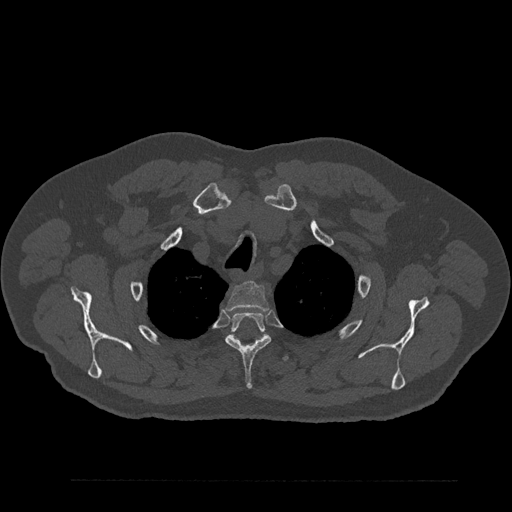
CT including the spine, one axial slice. Position 685 of 797 along the scan axis. Reconstruction kernel Br40s/3. 120 kVp. Bone window (W 1800 / L 400 HU). 0.5 mm slice thickness. 512 × 512 image matrix, field of view 430 × 430 mm. Male patient, age 61 years. From the clinical record (not read from this slice): primary cancer: prostate.
Annotated regions visible in this slice (semi-automatically segmented with operator editing):
- T2 vertebra: box from (x=226, y=281) to (x=268, y=311) px
- T3 vertebra: (x=225, y=312)–(x=271, y=389)
- T4 vertebra: (x=232, y=336)–(x=289, y=362)